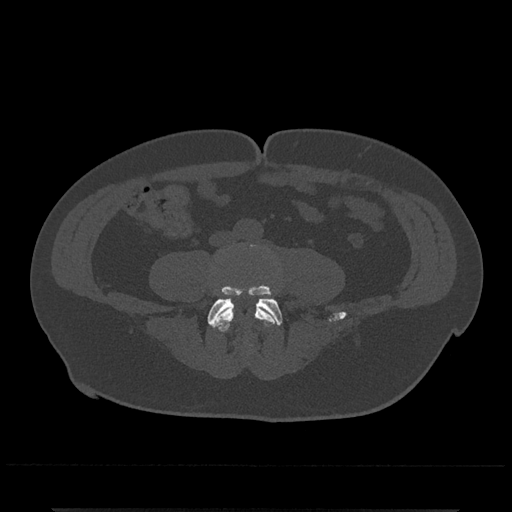
CT including the spine, one axial slice. Slice 117 of 797 in the series (ordered by position). Reconstruction kernel Br40s/3. 120 kVp. Bone window (W 1800 / L 400 HU). 0.5 mm slice thickness. 512 × 512 image matrix, field of view 393 × 393 mm. Patient: male, 67 years. Case-level facts recorded for this patient, not image findings: primary cancer: prostate.
Outlined on this slice (semi-automatically segmented with operator editing):
- L4 vertebra: bounding box [x1, y1, x2, y2] px = [212, 302, 280, 348]
- L5 vertebra: [207, 286, 283, 326]